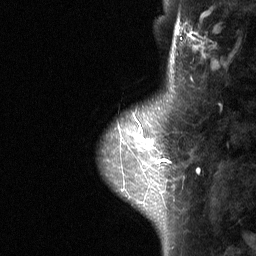
Breast MRI (dynamic contrast-enhanced), one sagittal slice; position 14 of 64 along the scan axis; dynamic contrast-enhanced study with each time point stored as its own series, time point 2 of 3 at this slice position (early post-contrast, ordered by acquisition time); 1.5 T; TE 4.8 ms, TR 27 ms; 256 × 256 image matrix, field of view 180 × 180 mm. Patient: female, 42 years. From the clinical record (not read from this slice): setting: breast cancer imaged before/during neoadjuvant chemotherapy; receptor status: triple-negative.
Outlined on this slice (semi-automatically segmented with operator editing):
- analysis volume of interest (the breast-tissue region the enhancement analysis was run in; not a lesion): bounding box [x1, y1, x2, y2] px = [111, 104, 178, 178]
- tumour enhancement mask (voxels above the 90 % enhancement threshold inside the analysis volume of interest): [151, 141, 170, 162]